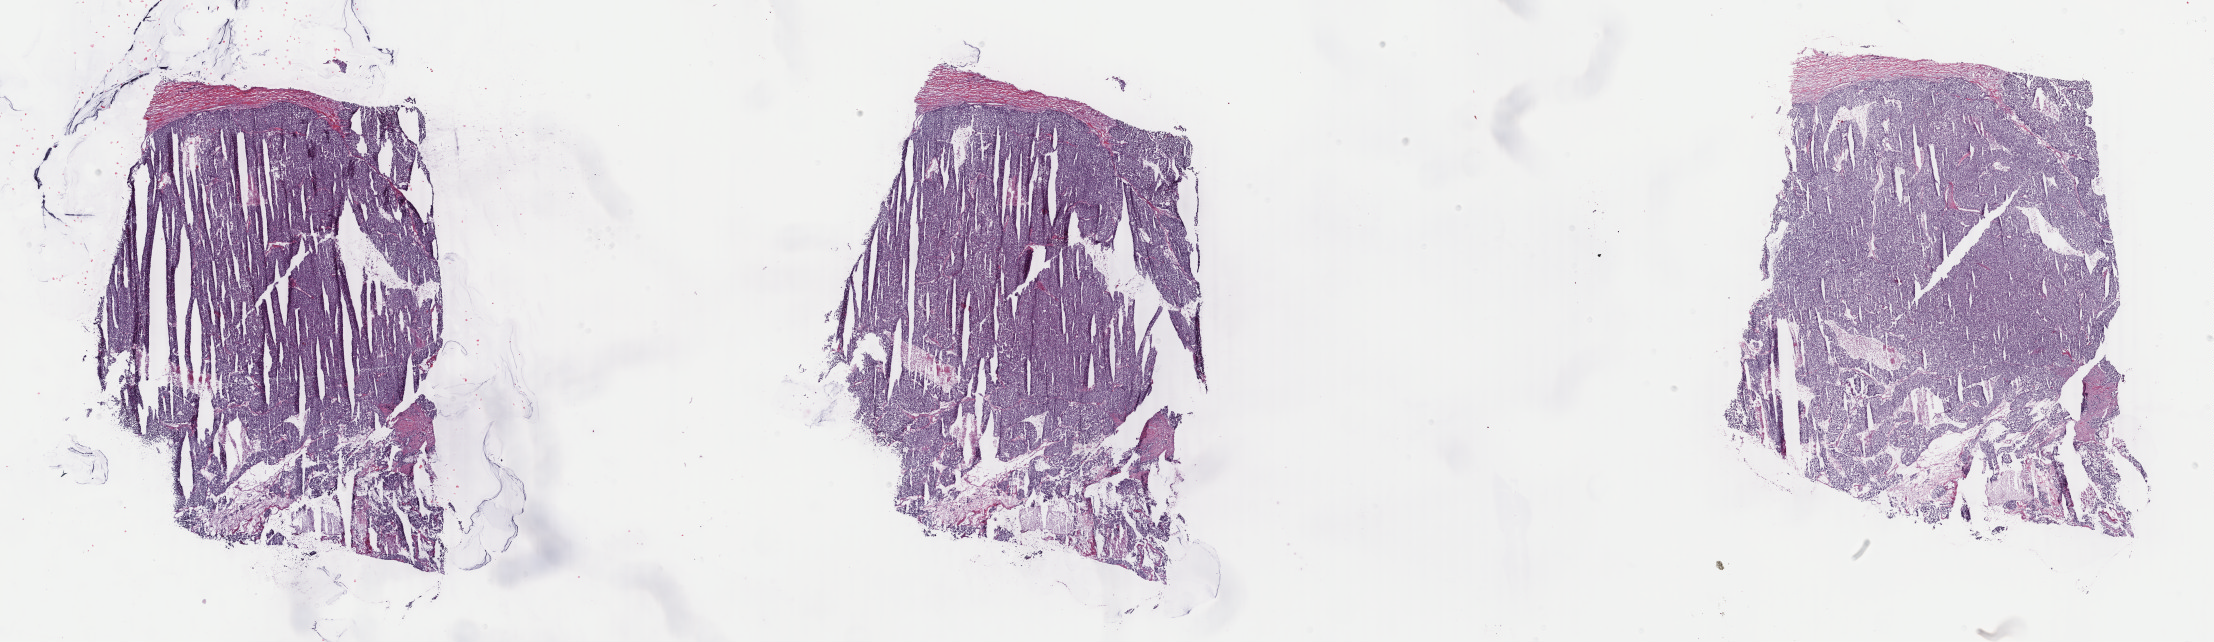
Digitized H&E-stained tissue section (whole slide) — whole scanned area (about 35.2 x 10.2 mm, acquisition: 40x scan) shown as a low-resolution overview; frozen section; primary tumour sample from the breast. Female, age 62 years at initial diagnosis. Pathologist review of this section (percent, as recorded): tumour cells 87%, tumour nuclei 90%, normal cells 0%, stromal cells 10%, necrosis 3%. Inflammatory infiltration, as recorded: lymphocyte infiltration 1%, monocyte infiltration 0%, neutrophil infiltration 0%.
Lymph nodes positive (case pathology): 0 of 8 examined. Histologic diagnosis: Infiltrating duct carcinoma, NOS. AJCC pathologic stage: IIA. TNM: T2 N0 M0.